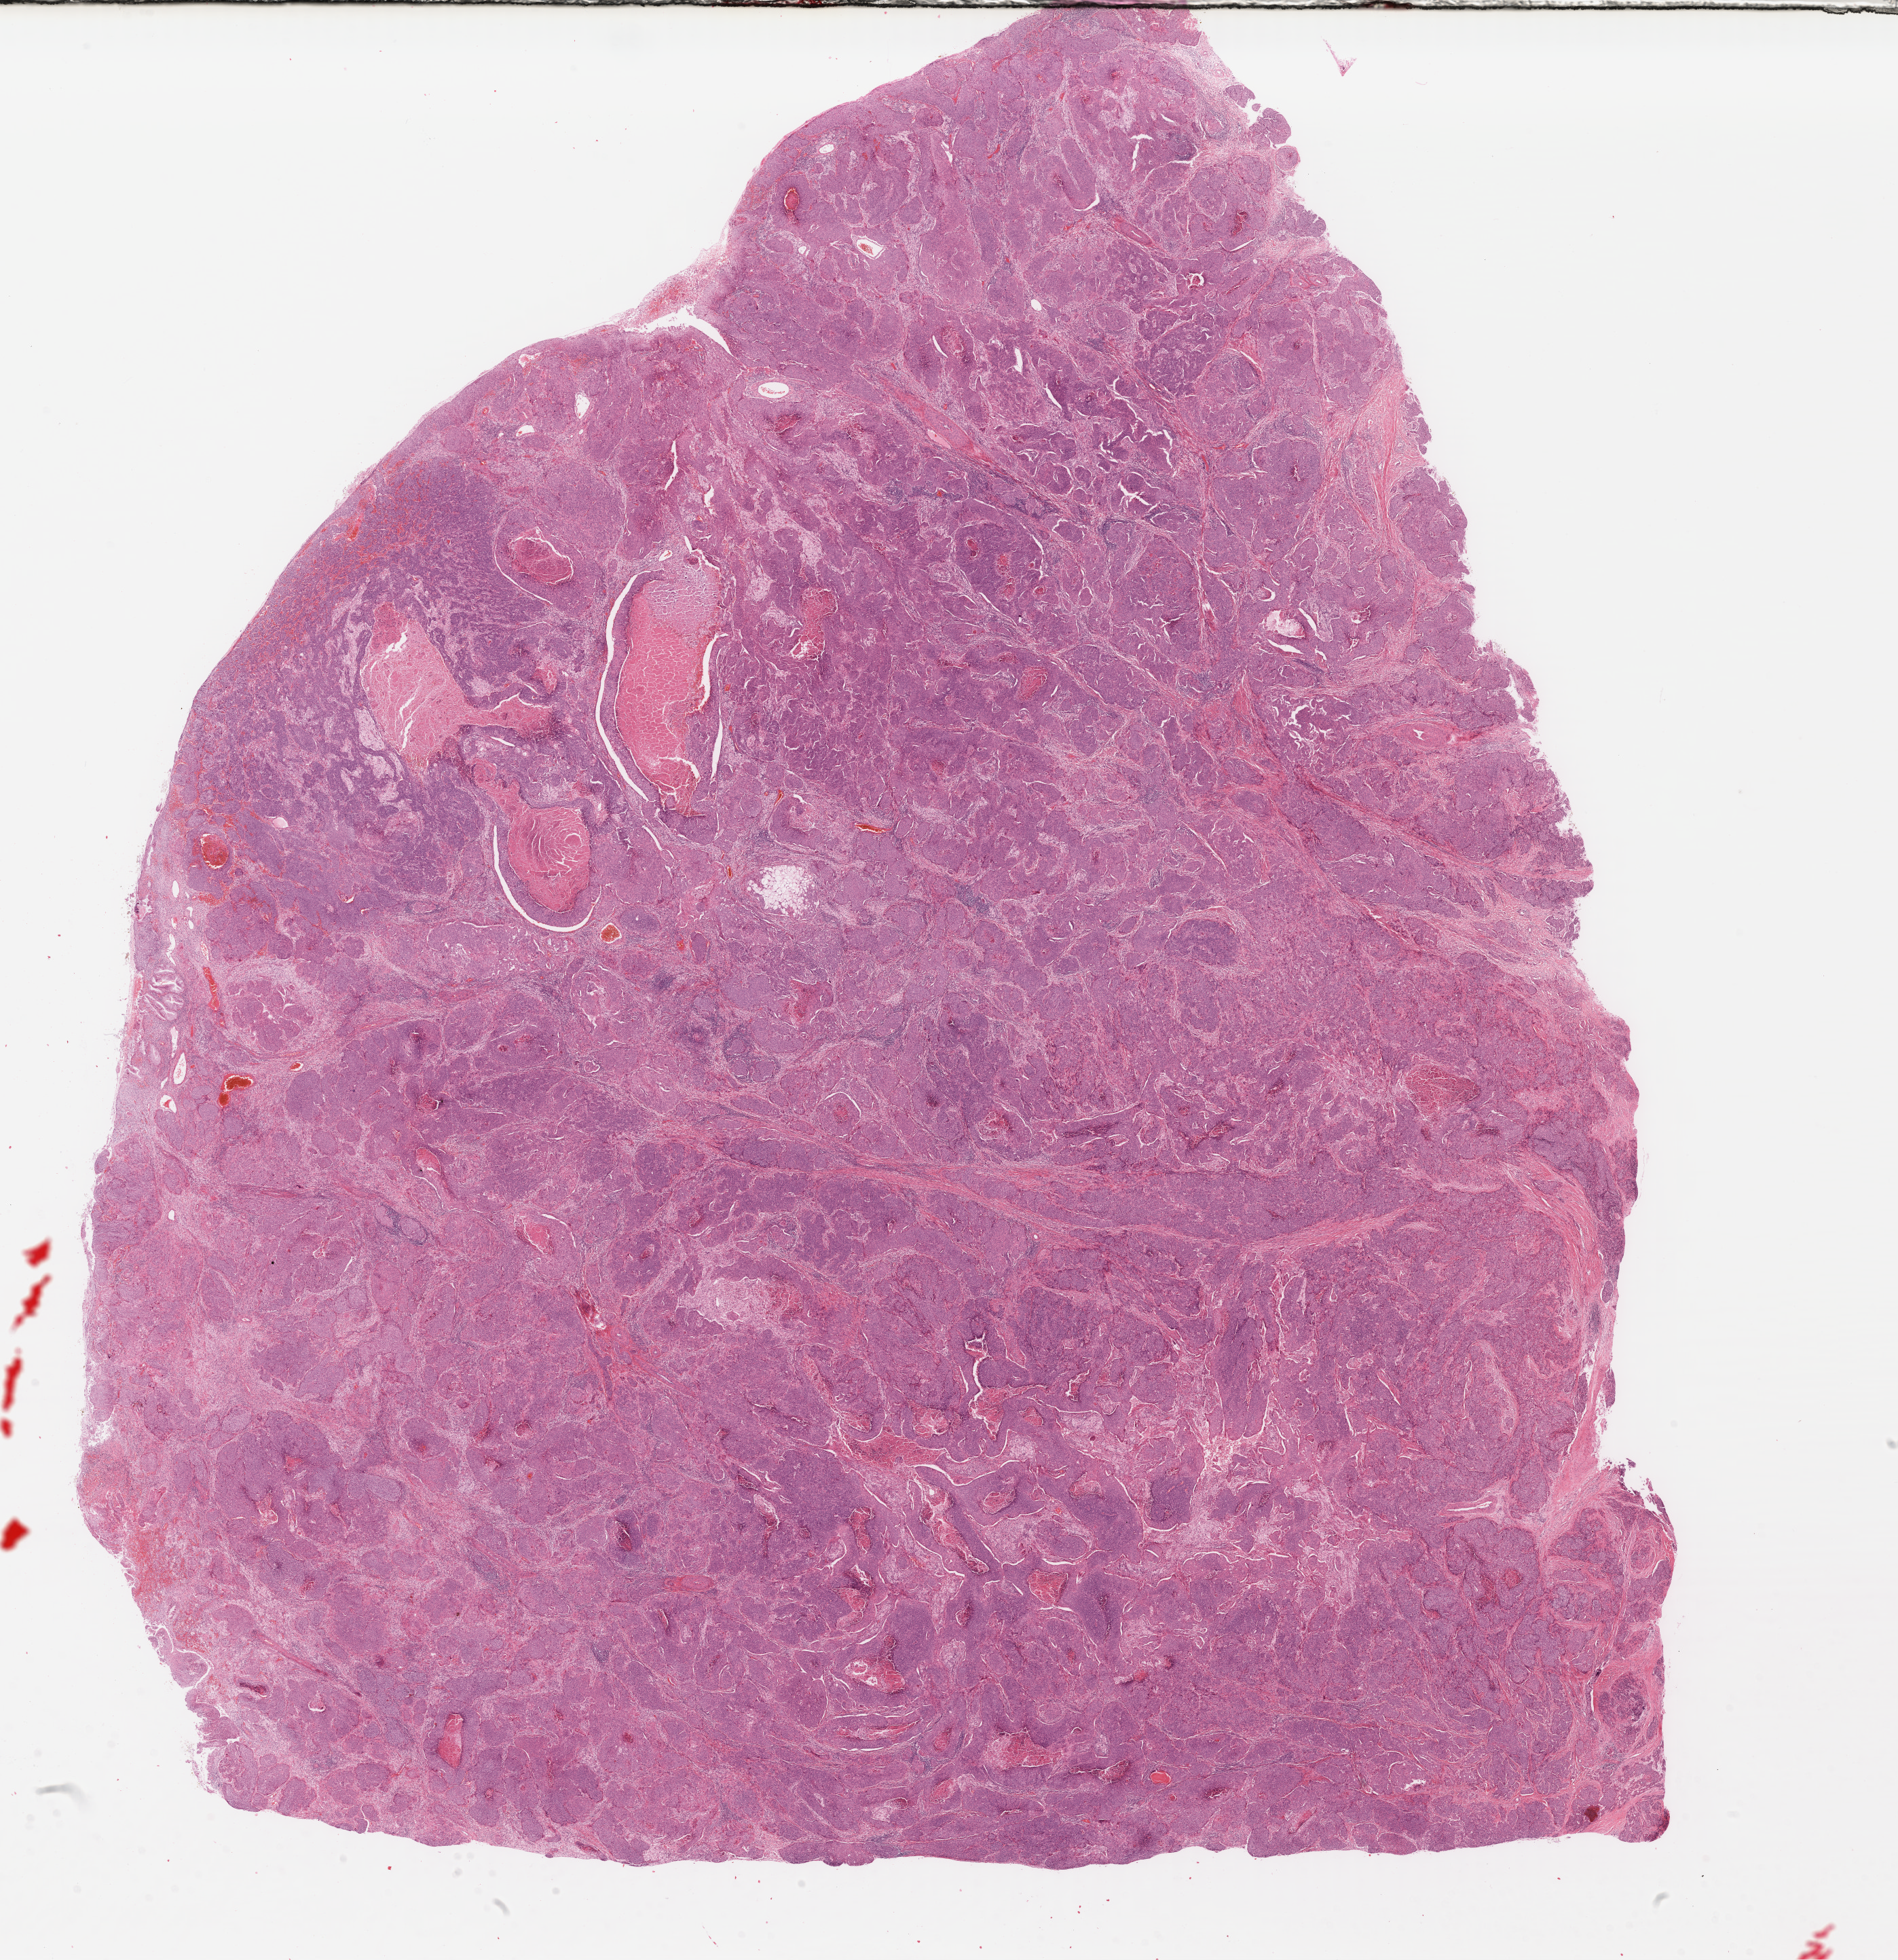
Hematoxylin and eosin (H&E) stained whole-slide image — shown as a low-resolution overview of the whole scanned area (about 22.0 x 22.7 mm, acquisition: 40x scan), FFPE section, sample: primary tumour, cervix. Female, age 31 years at initial diagnosis. Histologic grade: G2 (moderately differentiated).
FIGO stage: IIIB. Diagnosis: Squamous cell carcinoma, NOS.